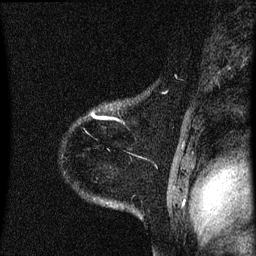
Breast MRI (dynamic contrast-enhanced), one sagittal slice. Position 54 of 60 along the scan axis. Dynamic contrast-enhanced series, image 2 of 3 at this slice position (ordered by acquisition). 1.5 T. TE 4.2 ms, TR 8.4 ms. 256 × 256 image matrix. Female patient, age 35 years. Case-level facts recorded for this patient, not image findings: setting: breast cancer imaged before/during neoadjuvant chemotherapy; receptor status: HER2-positive.
Outlined on this slice (semi-automatic segmentation, software-assisted and operator-edited):
- analysis volume of interest (the breast-tissue region the enhancement analysis was run in; not a lesion): bounding box <63,90,174,173> (left, top, right, bottom; pixels)
- tumour enhancement mask (voxels above the 70 % enhancement threshold inside the analysis volume of interest): <91,112,120,121>